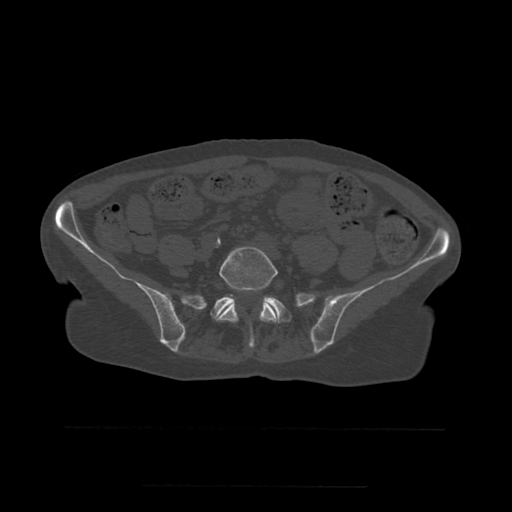
CT including the spine, one axial slice. Position 139 of 544 along the scan axis. Bone window (W 1800 / L 400 HU). 1.25 mm slice thickness. 512 × 512 image matrix. Patient age 58 years. Case-level facts recorded for this patient, not image findings: primary cancer: lung.
Outlined on this slice (semi-automatically segmented with operator editing):
- L5 vertebra: bounding box (x1, y1, x2, y2) in pixels: (216, 247, 279, 348)